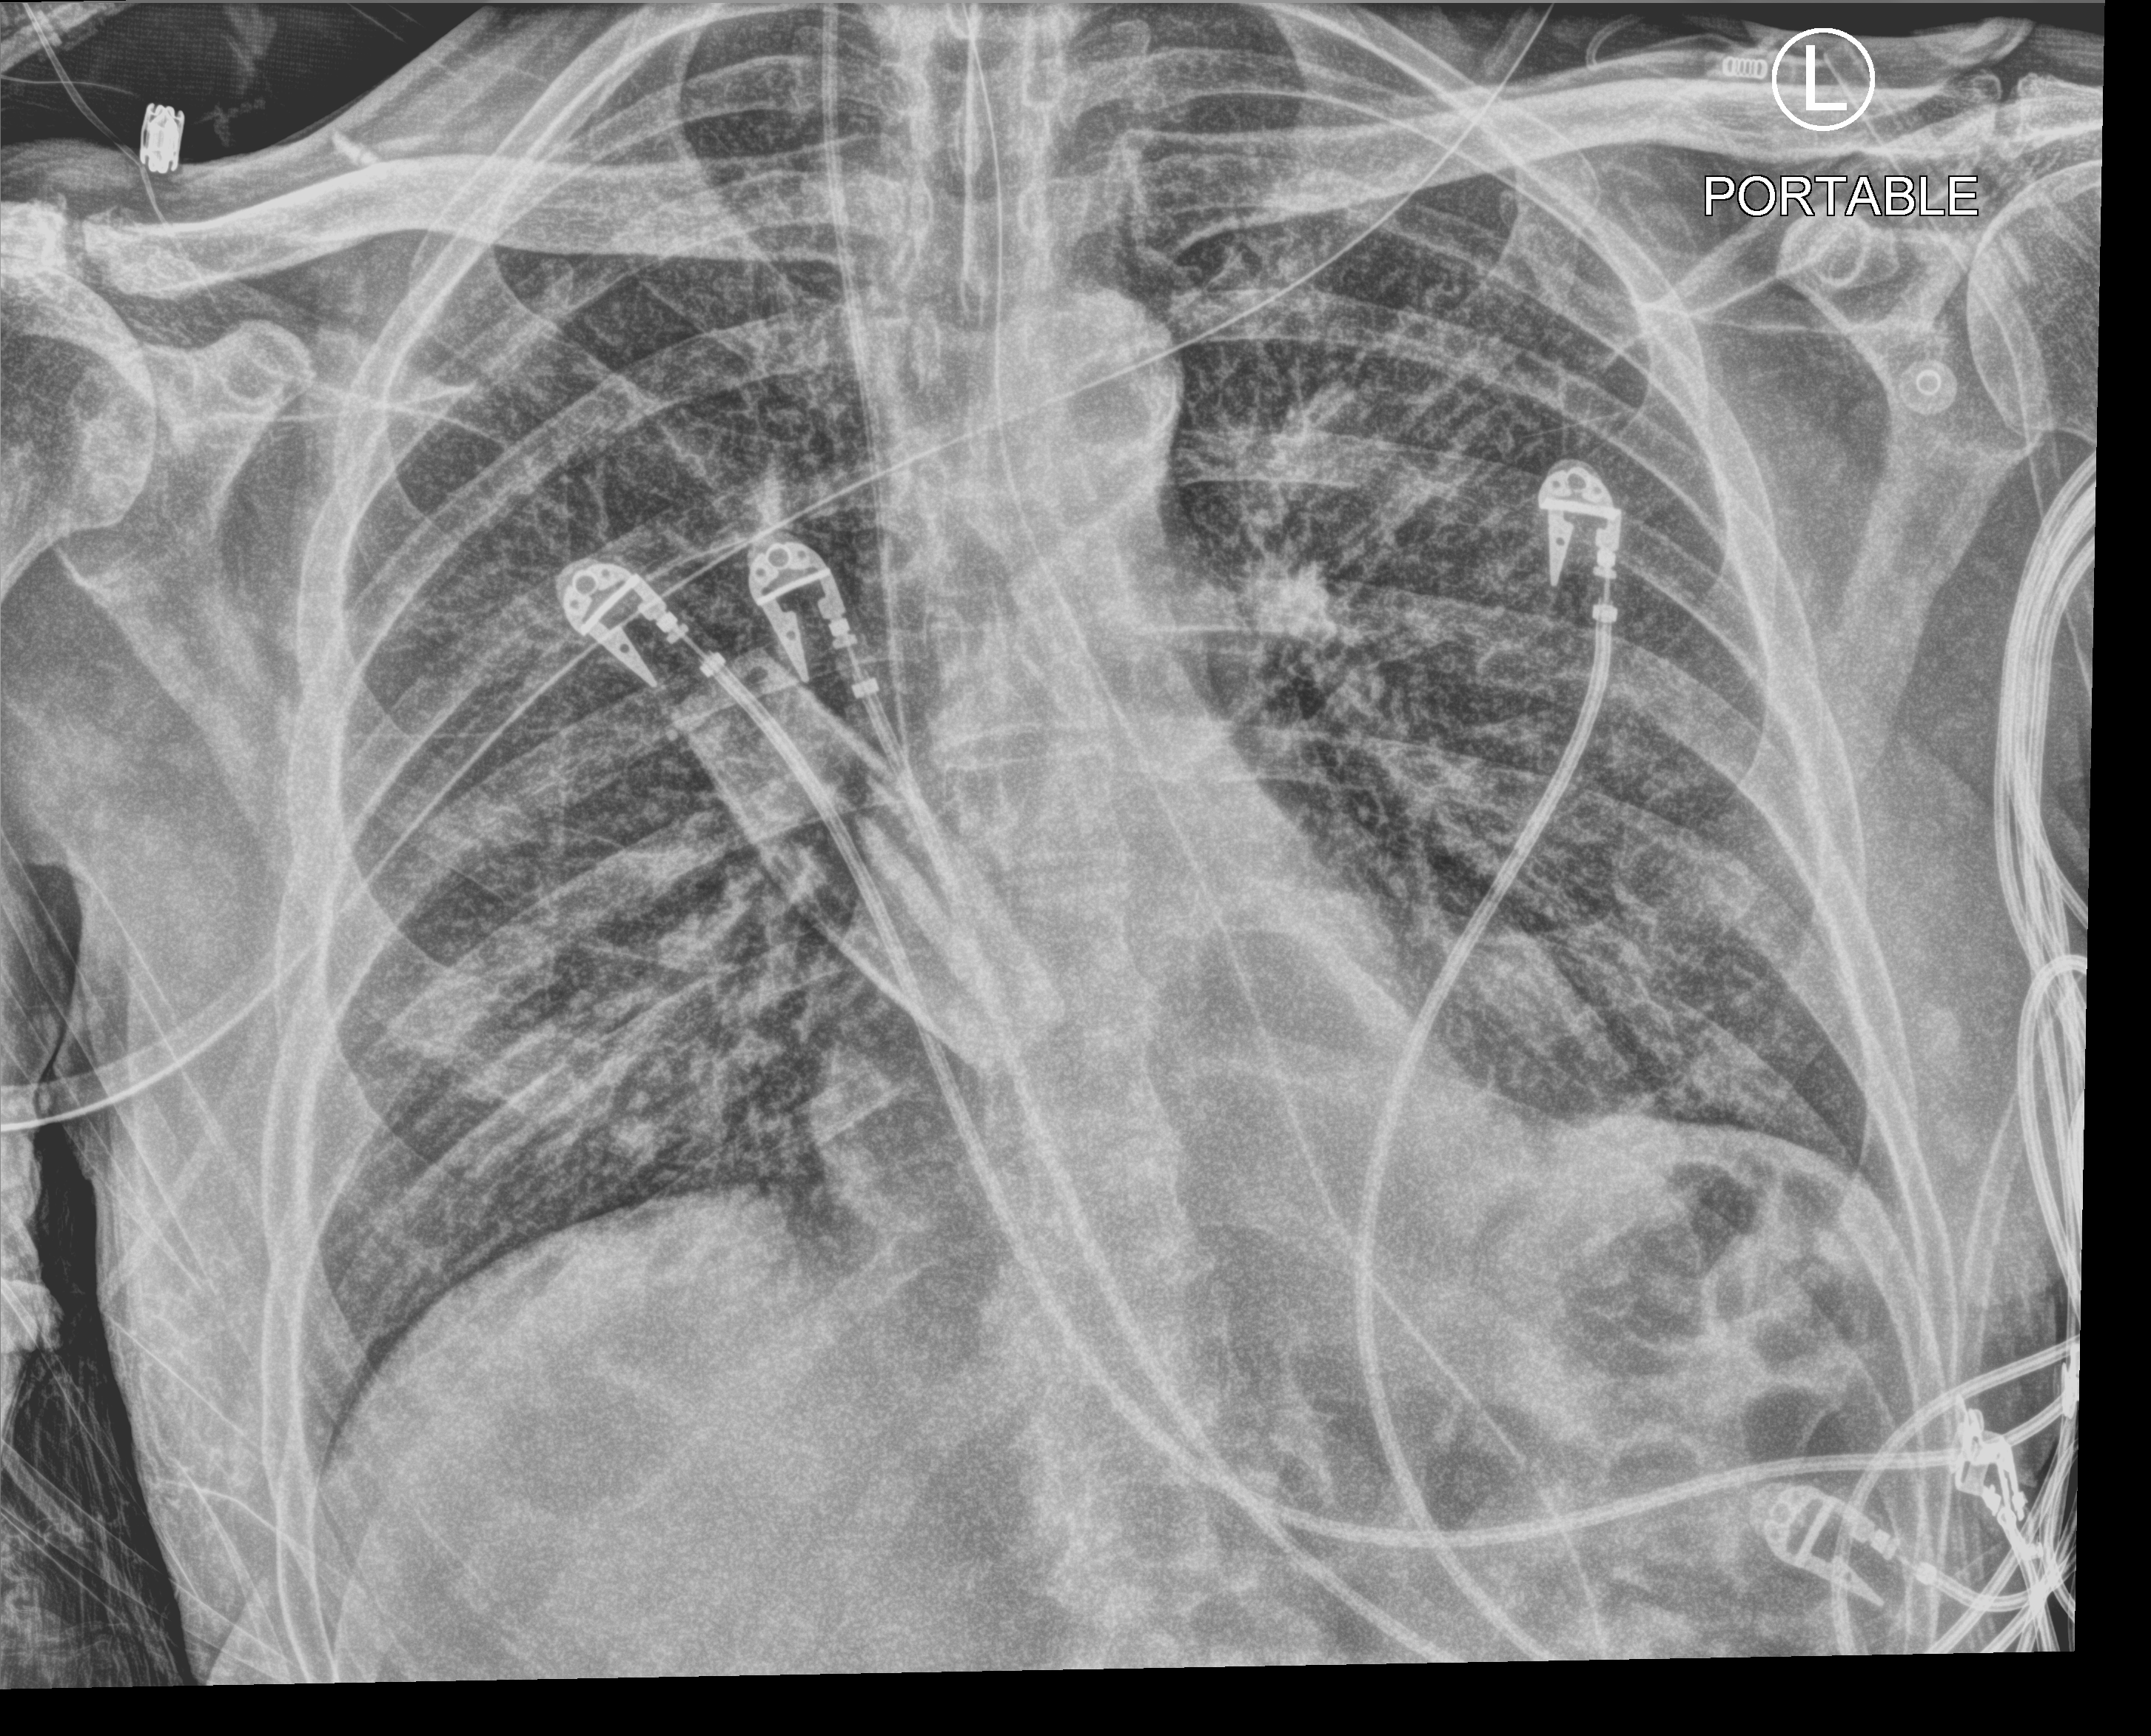
Chest X-ray (portable), anteroposterior (AP) projection. Patient hospitalised with COVID-19; male, aged 75–90 years.
Hospital-stay facts (about this admission, not read from this image; timing relative to this image not recorded): diabetes (admission record): yes.